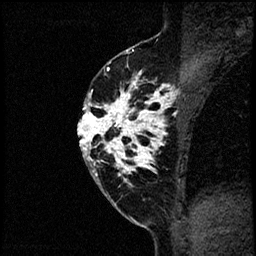
Breast MRI (dynamic contrast-enhanced), one sagittal slice; dynamic contrast-enhanced study with each time point stored as its own series, time point 2 of 4 at this slice position (early post-contrast, ordered by acquisition time); 1.5 T; TE 4.2 ms, TR 17.6 ms; 2 mm slice thickness; 256 × 256 image matrix, field of view 200 × 200 mm. Patient: female, 40 years. Case-level facts recorded for this patient, not image findings: setting: breast cancer imaged before/during neoadjuvant chemotherapy; receptor status: HER2-positive.
Outlined on this slice (semi-automatically segmented with operator editing):
- analysis volume of interest (the breast-tissue region the enhancement analysis was run in; not a lesion): bounding box [x1, y1, x2, y2] px = [79, 56, 197, 205]
- tumour enhancement mask (voxels above the 100 % enhancement threshold inside the analysis volume of interest): [79, 60, 197, 181]